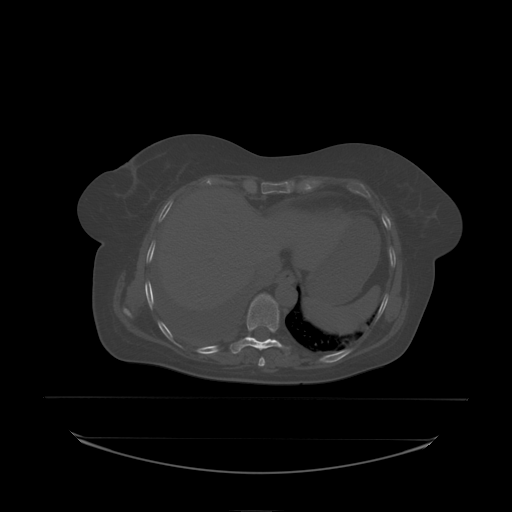
CT including the spine, one axial slice; slice 123 of 242 in the series (ordered by position); bone window (W 1800 / L 400 HU); 2.5 mm slice thickness; 512 × 512 image matrix, field of view 500 × 500 mm. Female patient, age 53 years. From the clinical record (not read from this slice): primary cancer: lung.
Annotated regions visible in this slice (semi-automatic segmentation, software-assisted and operator-edited):
- T9 vertebra: bounding box [x1, y1, x2, y2] px = [247, 295, 280, 338]